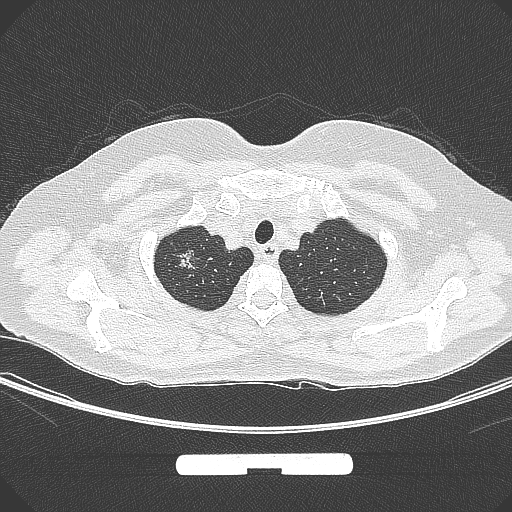
Chest CT, one axial slice. Slice 261 of 295 in the series (ordered by position). Lung window (W 1500 / L -600 HU). 512 × 512 image matrix, field of view 369 × 369 mm. Female patient, age 58 years. From the clinical record (not read from this slice): clinical TNM (as recorded): T1b N0 M0; histopathological grade: G2-3.
Outlined on this slice (bounding box drawn by a radiologist):
- lung tumour (recorded histology: adenocarcinoma): box from (x=171, y=242) to (x=197, y=279) px